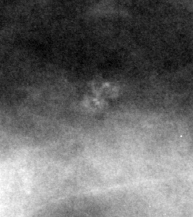
Cropped region of a digitized screen-film mammogram centred on a radiologist-marked abnormality, right breast, CC view, BI-RADS breast density category 3 (scale 1–4).
Marked abnormality: calcifications, morphology amorphous / pleomorphic, distribution clustered; BI-RADS assessment category 4; pathology result (as recorded, not read from the image): benign.